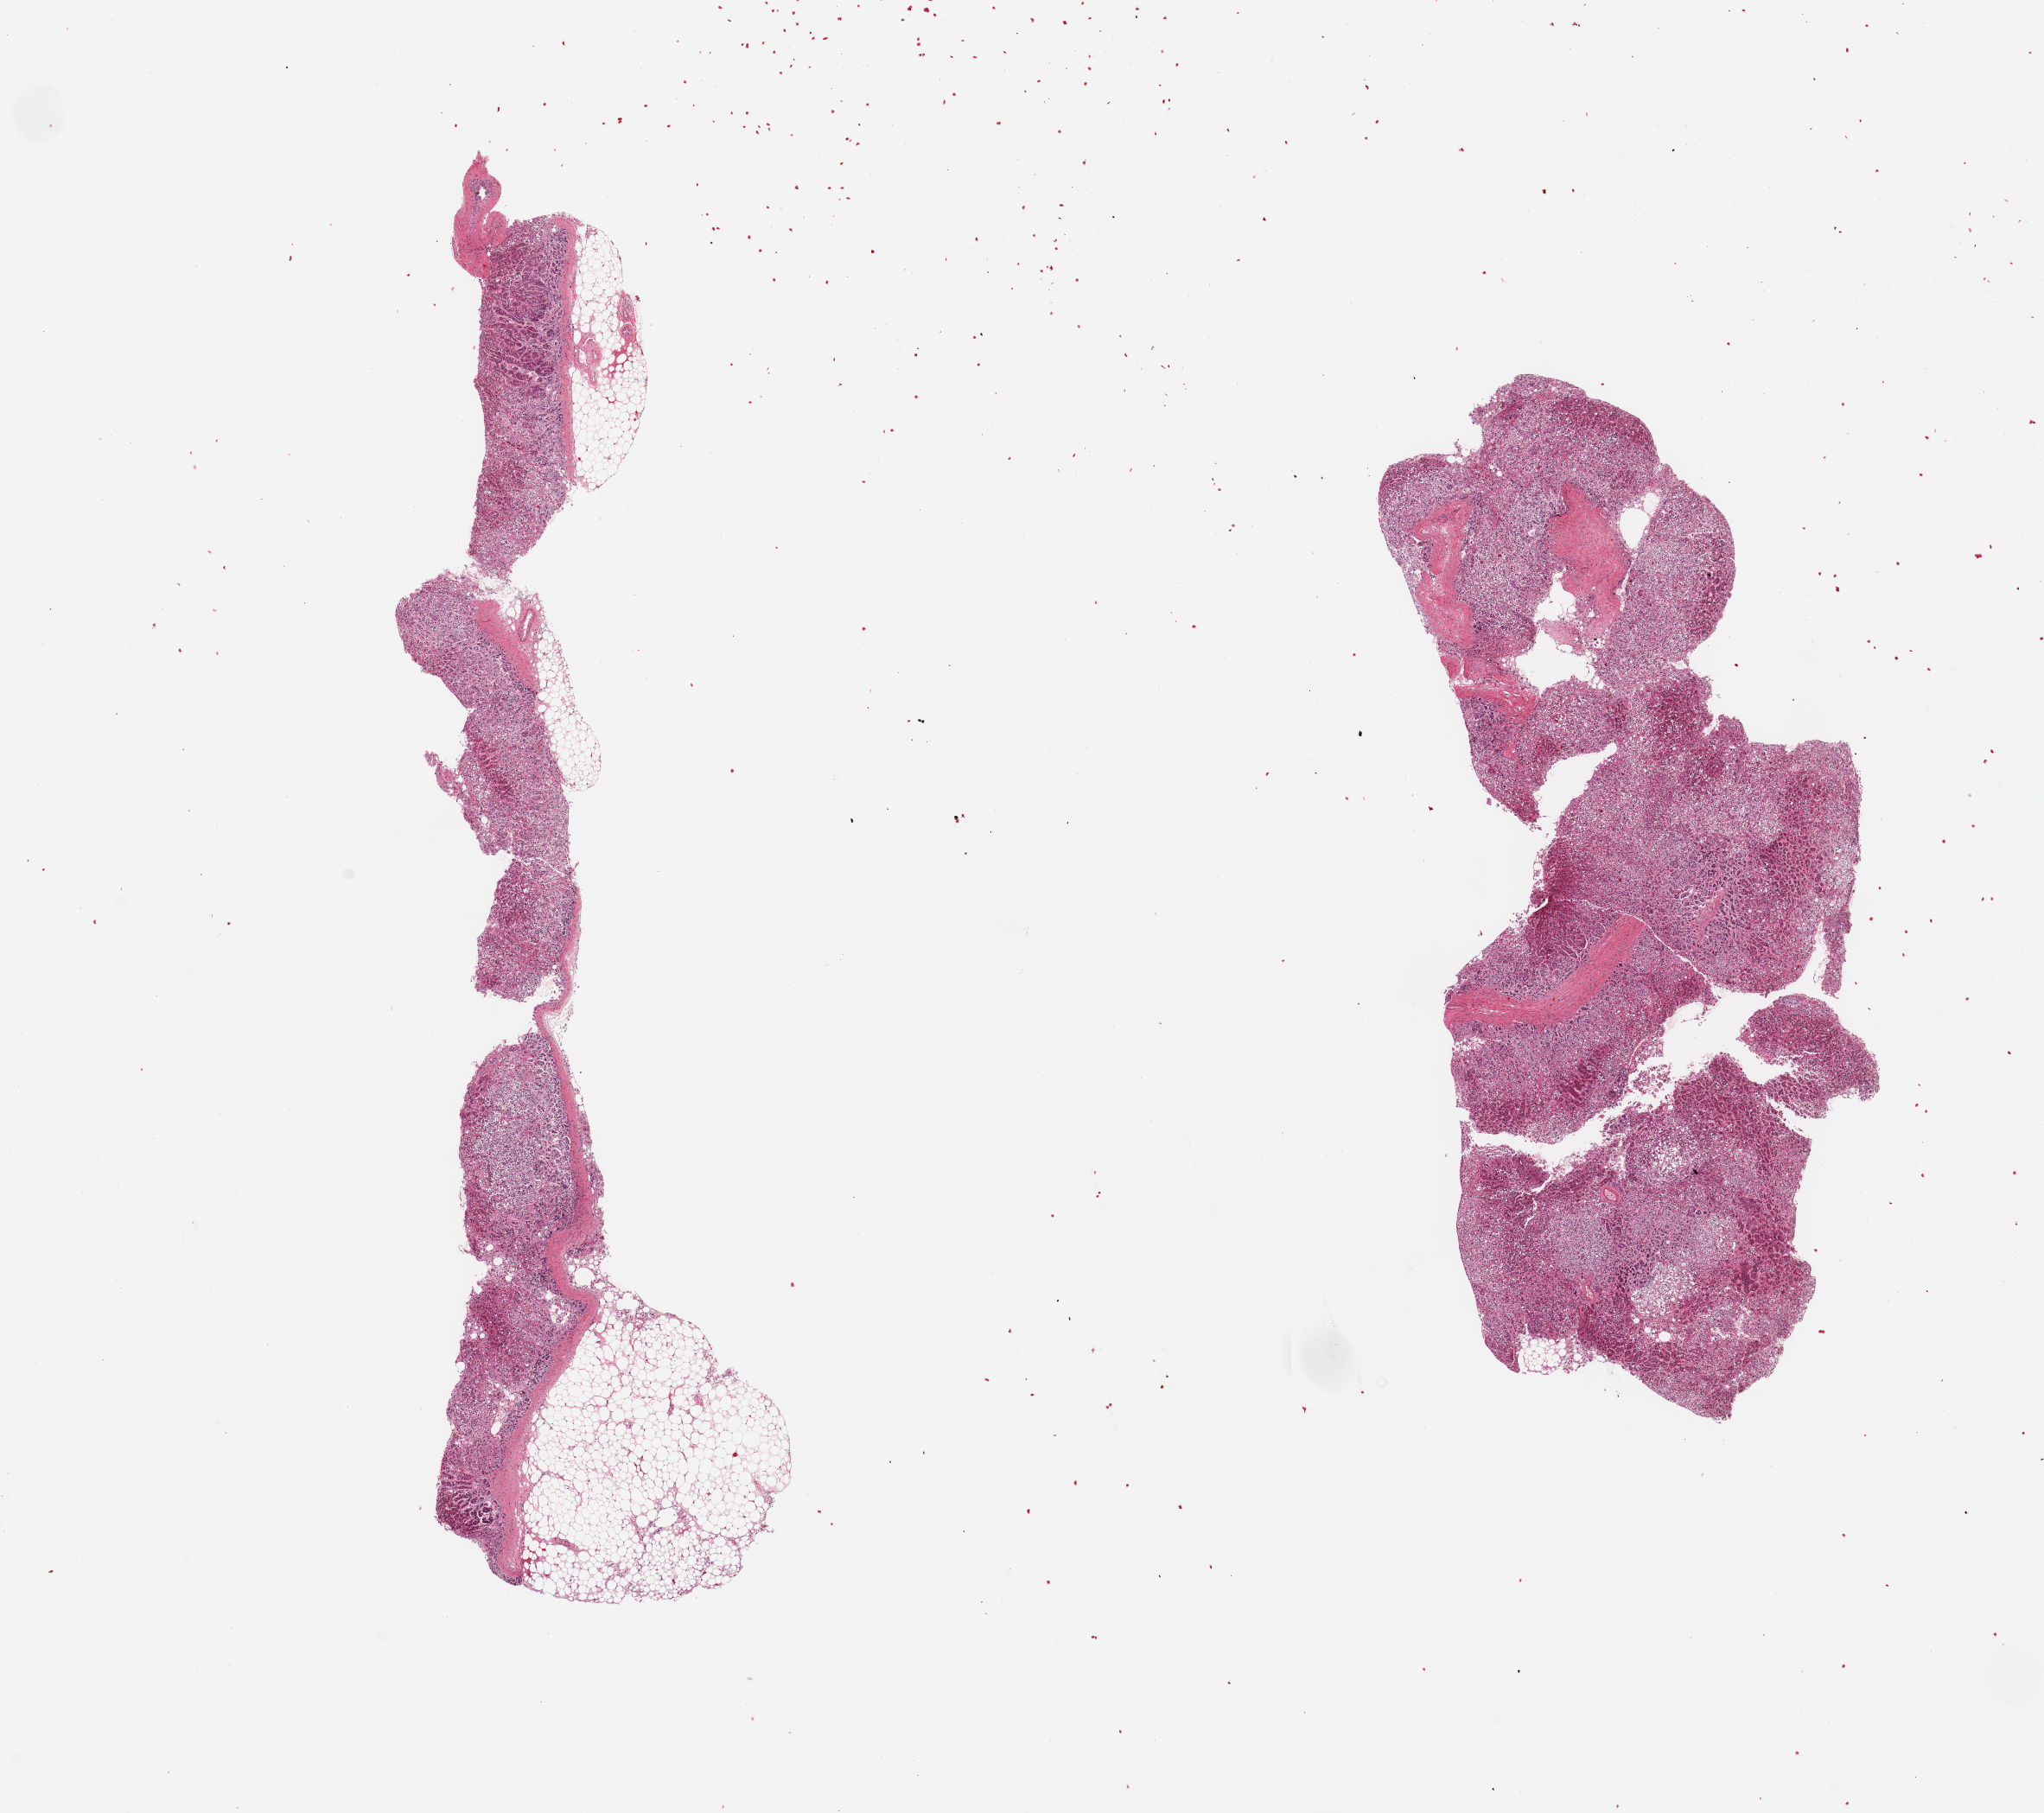
H&E whole-slide image — a low-resolution overview of the entire scanned area, about 18.7 x 16.6 mm (slide scanned at 20x), PAXgene-fixed paraffin-embedded (PFPE) section, target tissue: adrenal gland, donor tissue sample.
• review note (as recorded): 2 pieces; 1 piece is 40% external fat